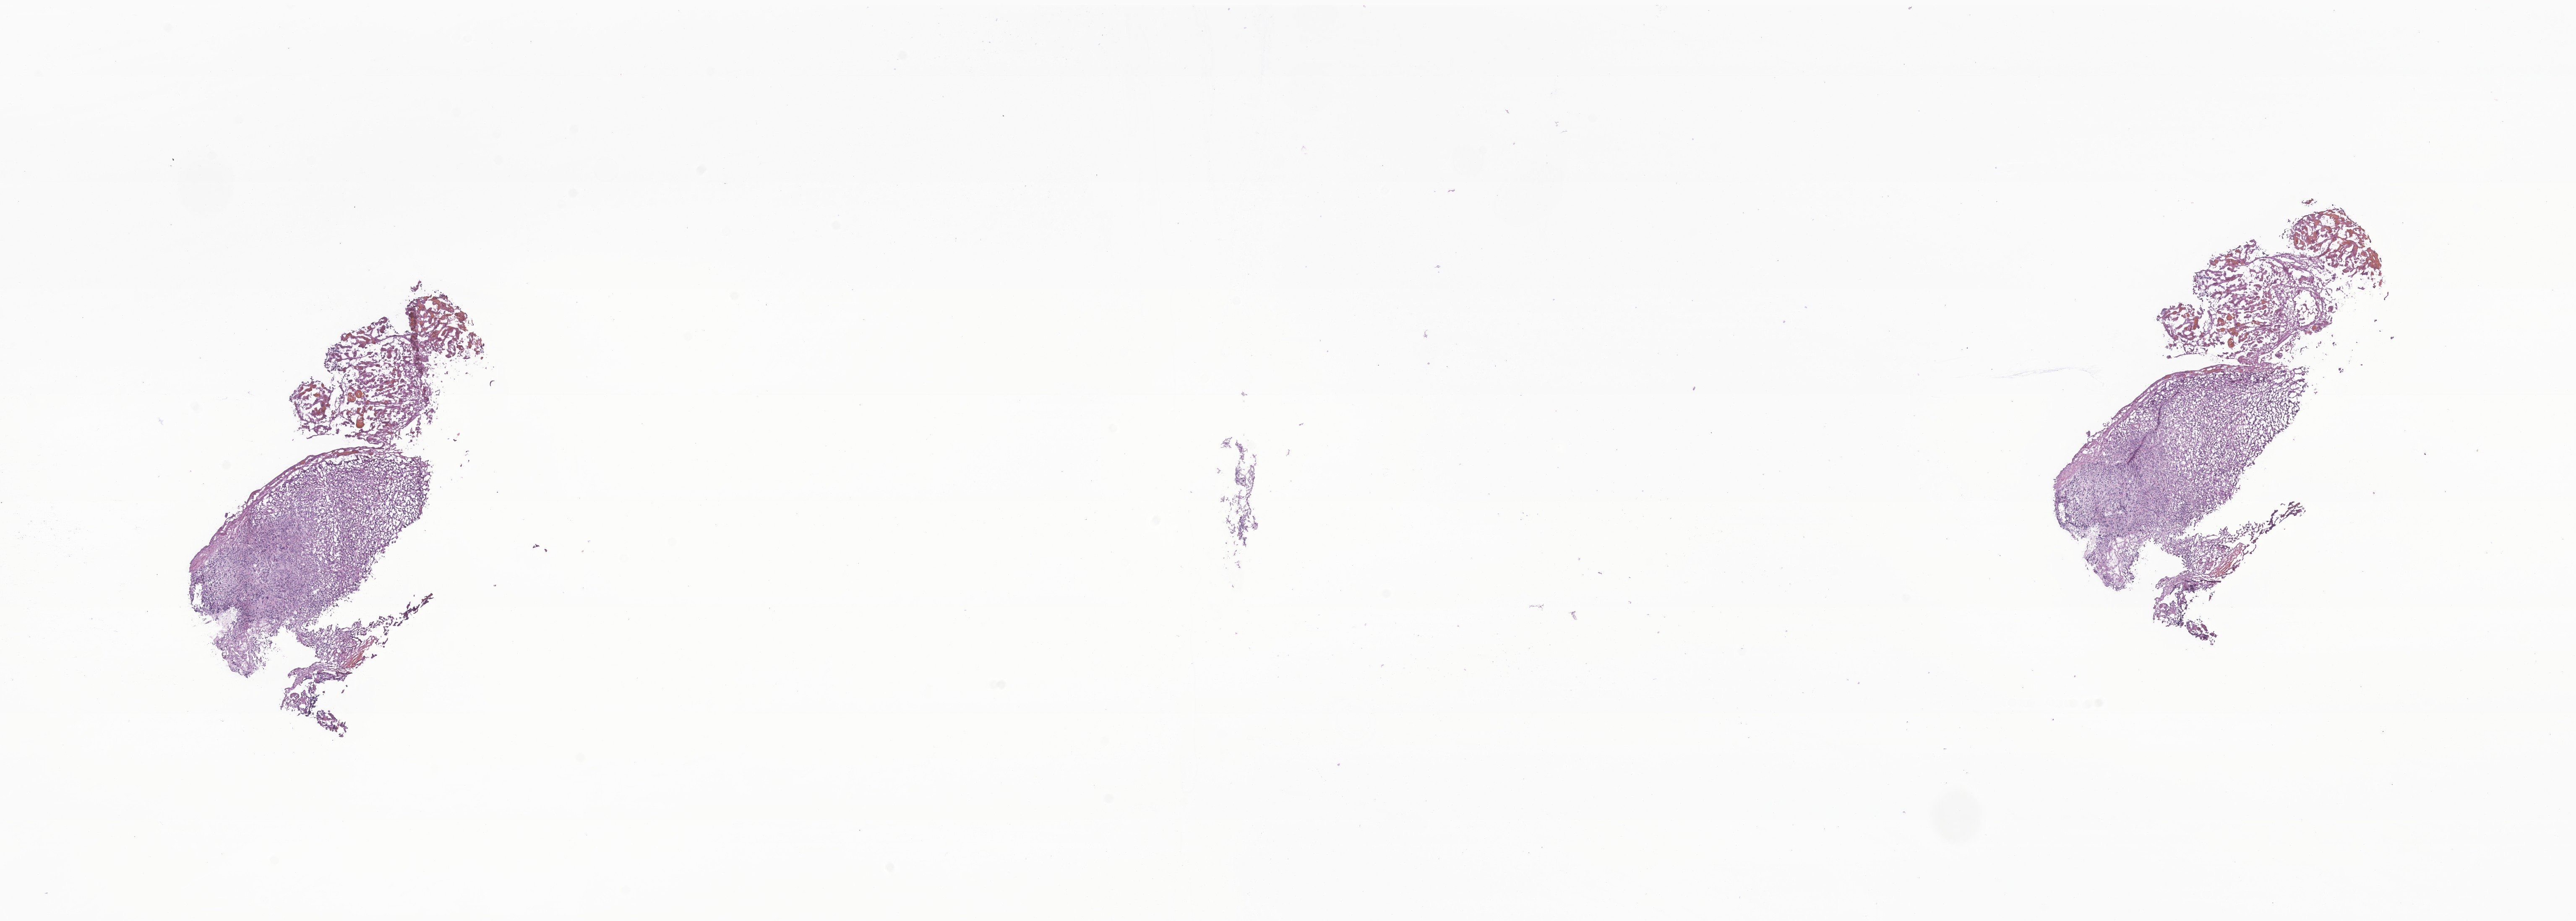
Digitized haematoxylin and eosin-stained section of tumor tissue from the brain, shown as a low-resolution overview of the whole scanned area (about 25.8 x 9.2 mm), cryosection (OCT / tissue freezing medium). Female patient, age 928 days (about 2.5 years).
Recorded diagnosis: Neoplasm, uncertain whether benign or malignant.